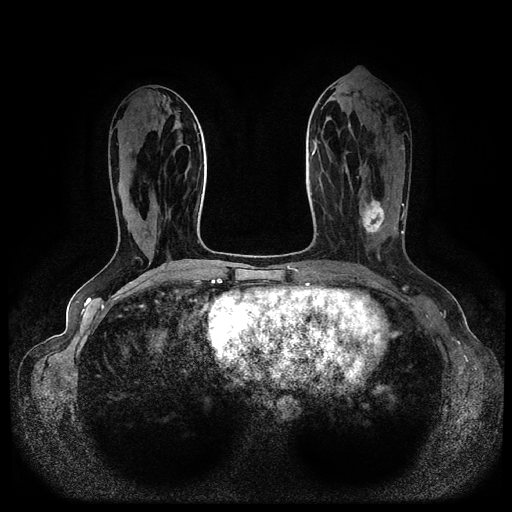
Breast MRI (dynamic contrast-enhanced, multi-phase), one axial slice. Slice 40 of 116 in the series (ordered by position). Dynamic contrast-enhanced series, time point 2 of 5 at this slice position (early post-contrast). 1.5 T. TE 2.6 ms, TR 5.3 ms. 2 mm slice thickness. 512 × 512 image matrix, field of view 350 × 350 mm. Patient: female, 45 years.
Outlined on this slice (semi-automatically segmented with operator editing):
- breast lesion (labelled 'tumour' in the annotation; benign lesions carry a separate 'benign' label): box from (x=359, y=191) to (x=390, y=240) px